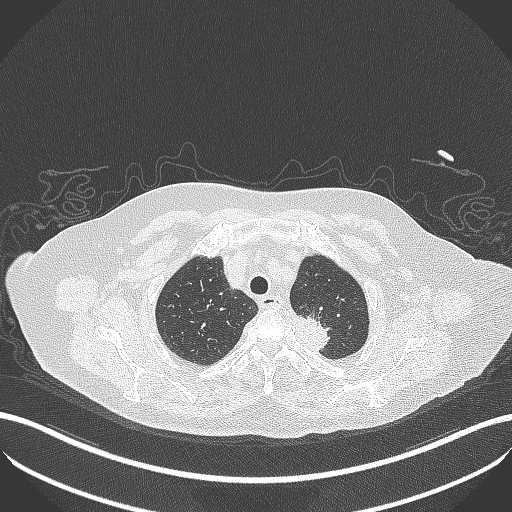
Chest CT, one axial slice; position 289 of 353 along the scan axis; reconstruction kernel B70f; 100 kVp; lung window (W 1500 / L -600 HU); 512 × 512 image matrix, field of view 400 × 400 mm. Female patient, age 81 years. Case-level facts recorded for this patient, not image findings: clinical TNM (as recorded): T2a N0 M0.
Annotated regions visible in this slice (bounding box drawn by a radiologist):
- lung tumour (recorded histology: adenocarcinoma): bounding box [x1, y1, x2, y2] px = [287, 309, 336, 358]